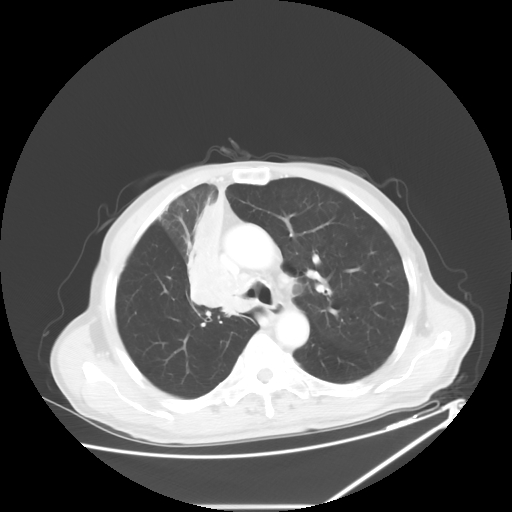
Chest CT, one axial slice. Slice 42 of 60 in the series (ordered by position). Reconstruction kernel STANDARD. Lung window (W 1500 / L -600 HU). 5 mm slice thickness. 512 × 512 image matrix, field of view 410 × 410 mm. Male patient, age 73 years. Case-level facts recorded for this patient, not image findings: clinical TNM (as recorded): T2a N1 M0.
Annotated regions visible in this slice (bounding box drawn by a radiologist):
- lung tumour (recorded histology: squamous cell carcinoma): bounding box <191,187,246,327> (left, top, right, bottom; pixels)